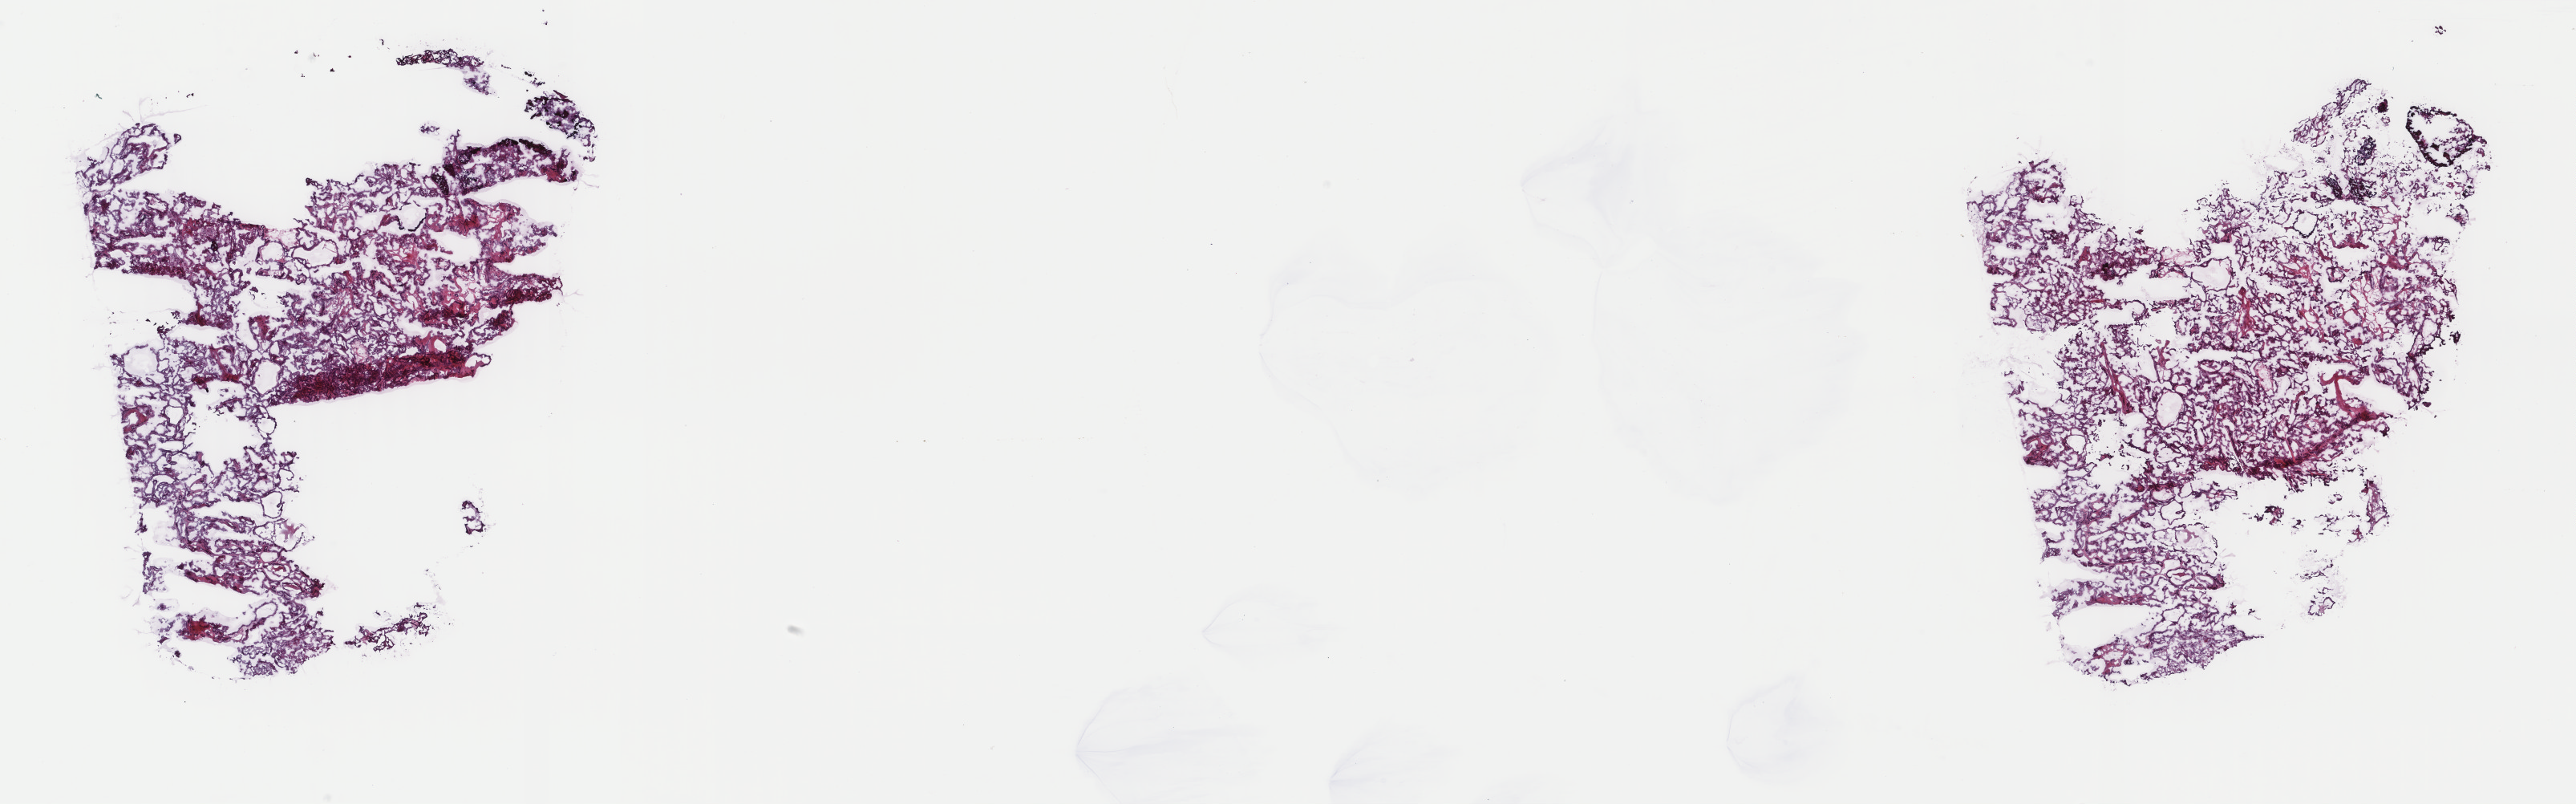
H&E whole-slide image, a low-resolution overview of the entire scanned area, about 25.5 x 8.0 mm (slide scanned at 40x), frozen section, sample: primary tumour, thyroid. Patient: female, age at initial diagnosis 46 years. Slide review estimates, as recorded: tumour cells 85%, tumour nuclei 85%, normal cells 0%, stromal cells 15%, necrosis 0%. Inflammatory infiltration, as recorded: lymphocyte infiltration 3%, monocyte infiltration 0%, neutrophil infiltration 0%.
- AJCC pathologic stage: IVA
- pathologic diagnosis: Papillary adenocarcinoma, NOS (thyroid gland)
- TNM: T4a N1 M0
- laterality: right
- lymph nodes positive (case pathology): 10 of 69 examined